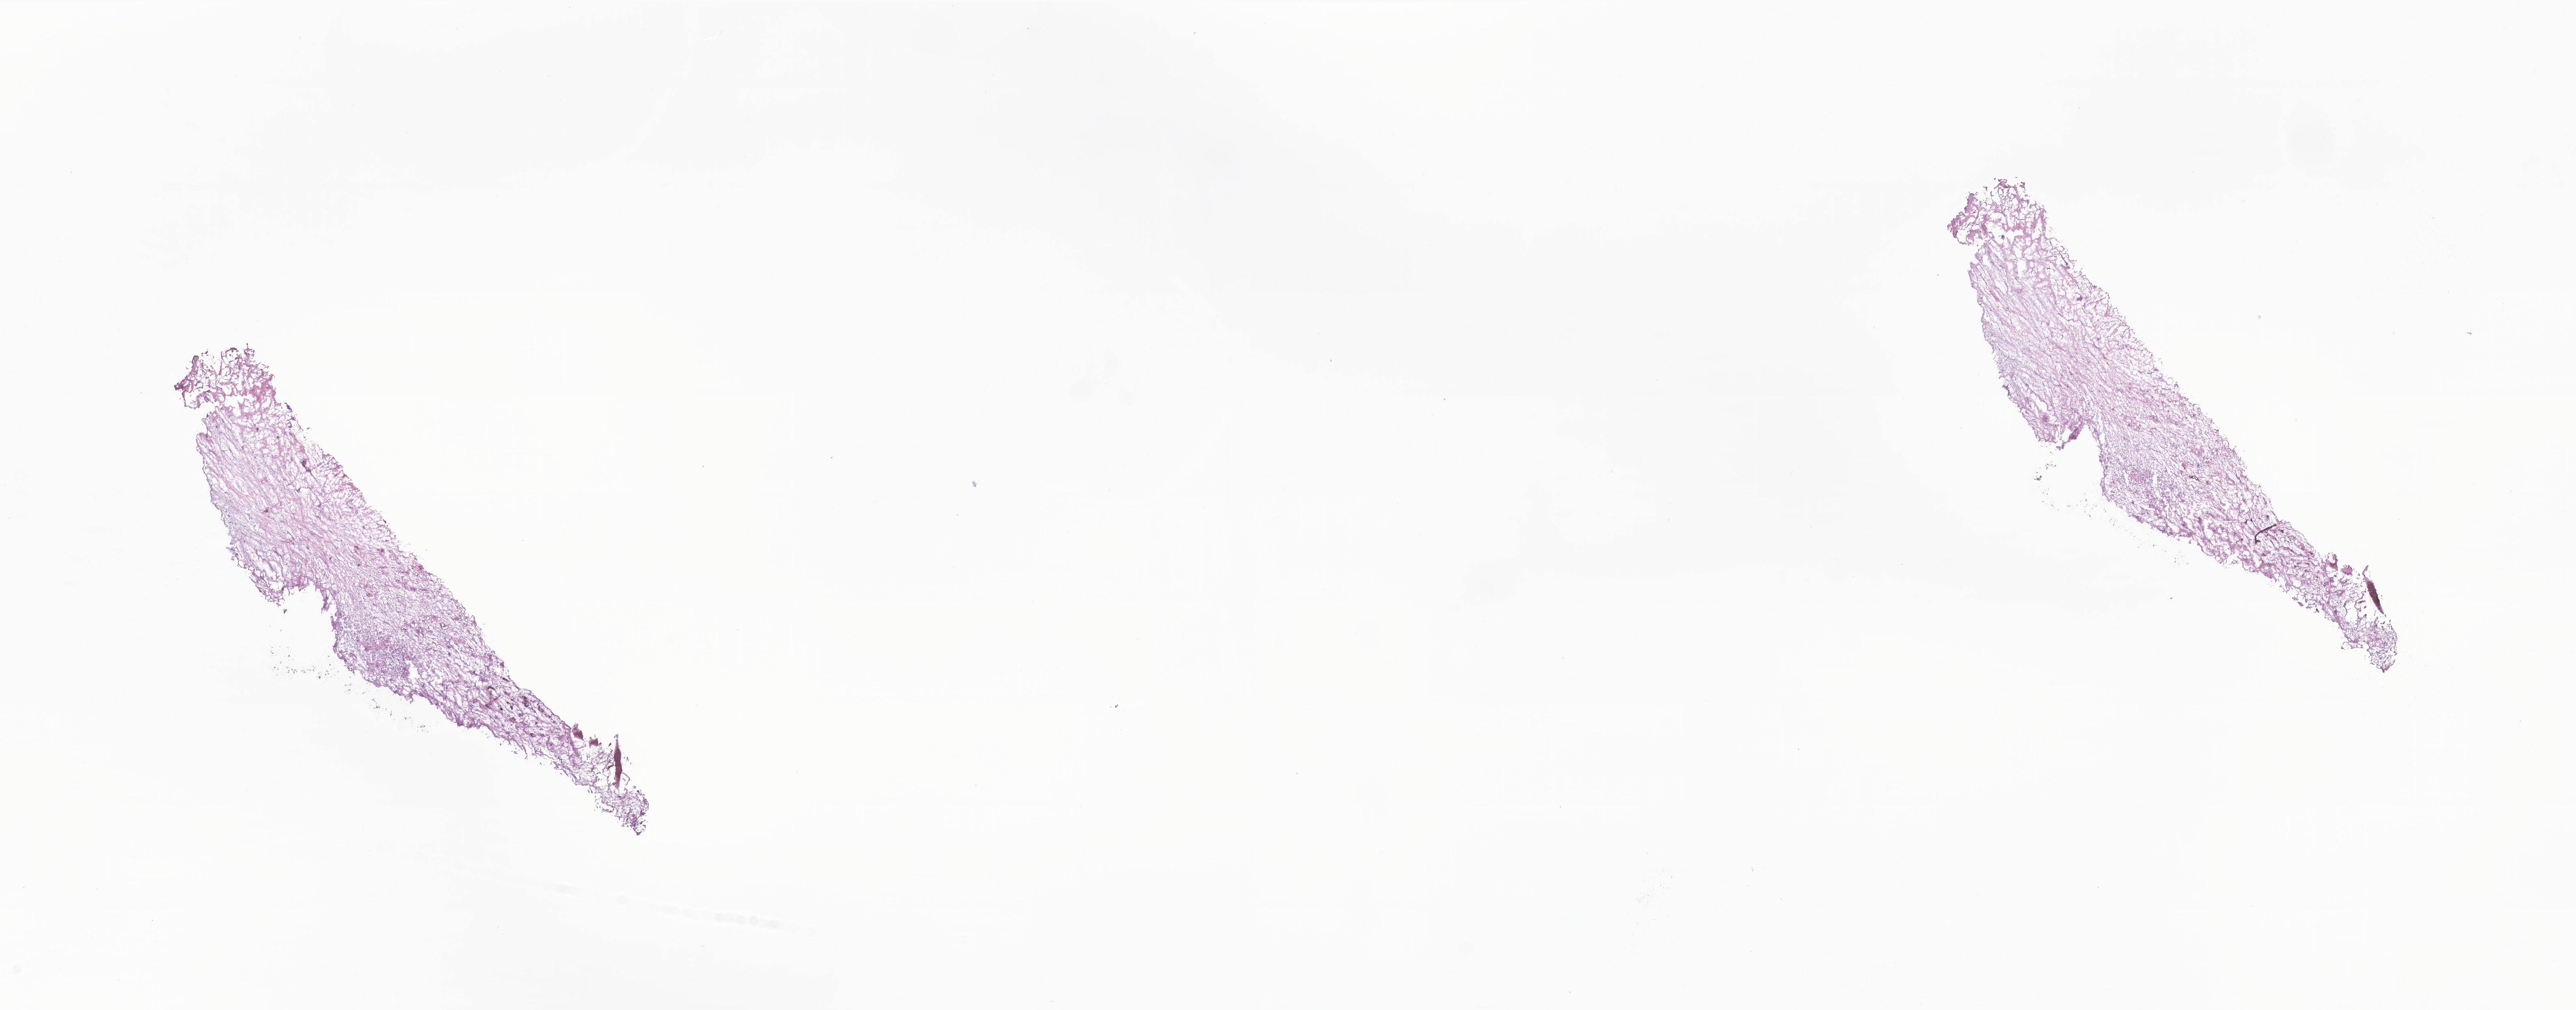
Digitized haematoxylin and eosin-stained section of tumor tissue from the cranial and/or facial bone, a low-resolution overview of the entire scanned area, about 26.8 x 10.5 mm. Cryosection (OCT / tissue freezing medium). Patient female; age 263 days.
Diagnosis (ICD-O-3 morphology term): Melanotic neuroectodermal tumor.